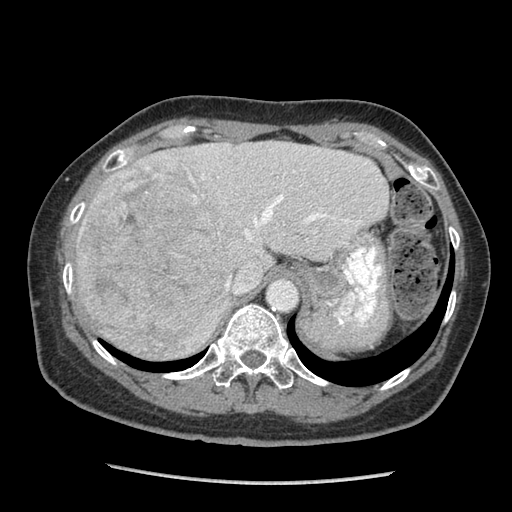
Contrast-enhanced abdominal CT (liver protocol), one axial slice; position 66 of 105 along the scan axis; reconstruction kernel STANDARD; soft-tissue window (W 400 / L 40 HU); 2.5 mm slice thickness; 512 × 512 image matrix, field of view 340 × 340 mm. Case-level facts recorded for this patient, not image findings: diagnosis: hepatocellular carcinoma (patient treated with transarterial chemoembolisation; whether this scan precedes or follows treatment is not stated here); TNM stage (as recorded): Stage-I; Child-Pugh class: A; tumour differentiation: moderately differentiated; tumour nodularity: uninodular.
Structures marked on this image (semi-automatically segmented with operator editing):
- abdominal aorta: box from (x=269, y=279) to (x=298, y=310) px
- liver parenchyma outside the tumour (the mass and vessels are separate outlines, so this box may not span the whole liver): (x=74, y=140)–(x=388, y=358)
- mass: (x=75, y=161)–(x=226, y=353)
- liver vessels: (x=196, y=151)–(x=366, y=293)